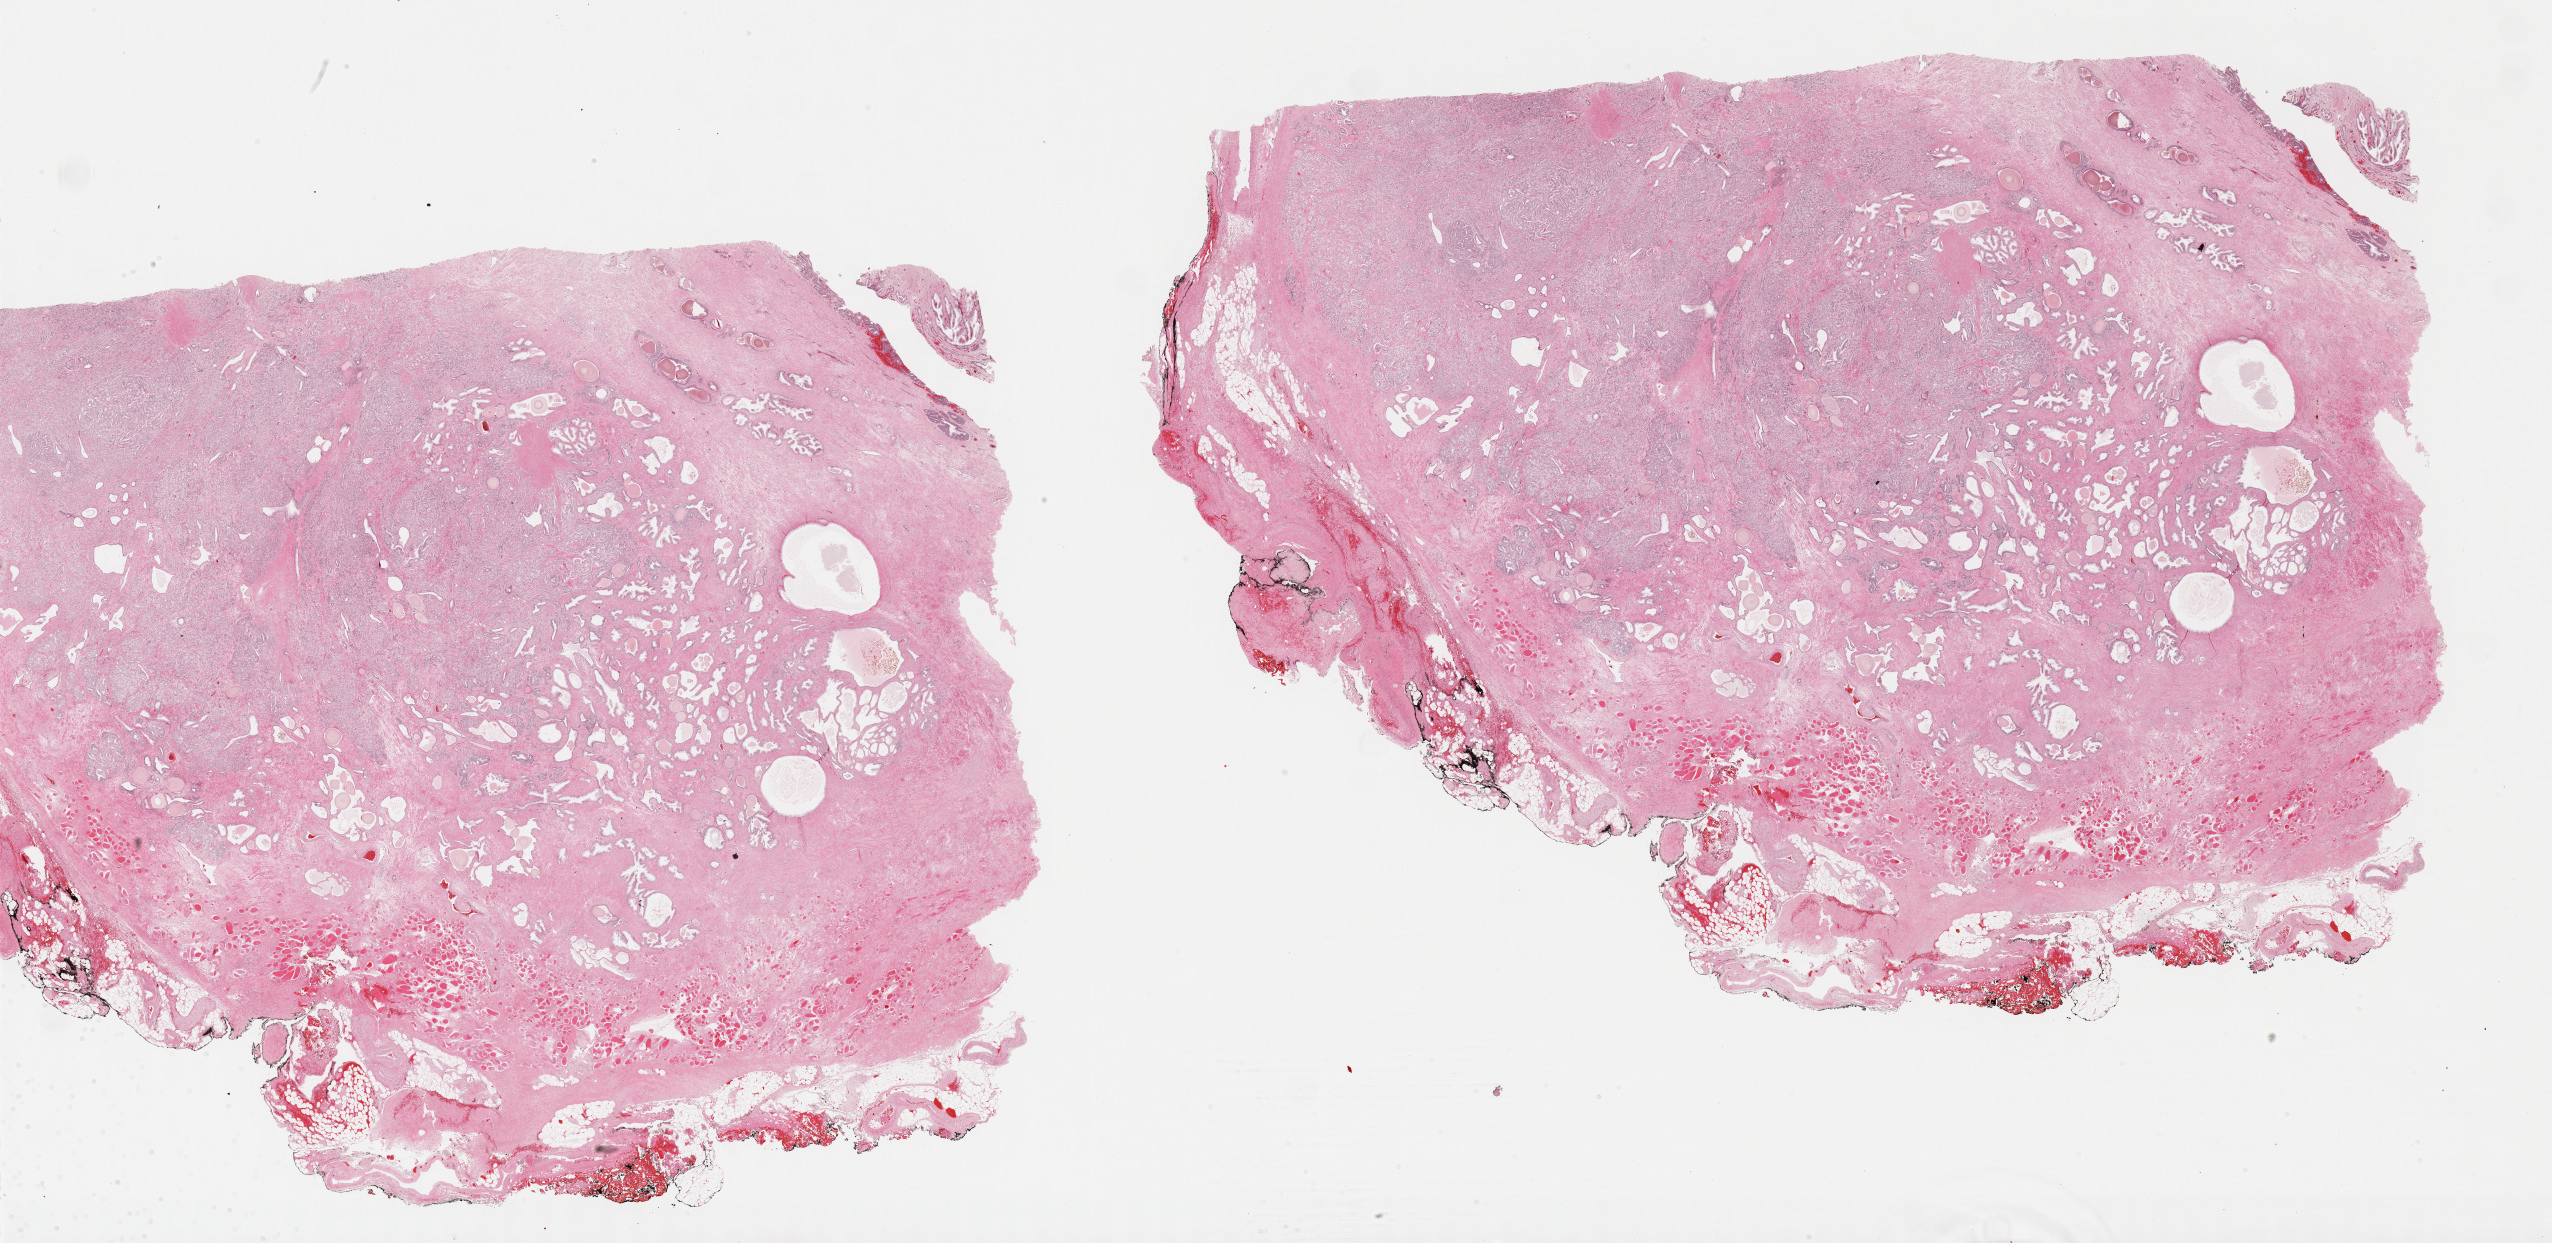
Whole-slide histology image, H&E-stained — low-resolution overview of the scanned area, about 41.3 x 20.1 mm (from a 40x scan); FFPE section; primary tumour sample from the prostate. Patient: male, age at initial diagnosis 65 years. Gleason score: 9 (4+5).
Pathologic diagnosis: Adenocarcinoma, NOS (prostate gland).